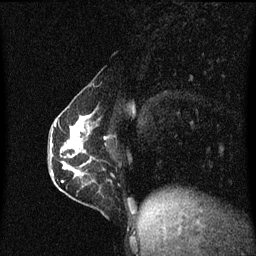
Breast MRI (dynamic contrast-enhanced), one sagittal slice; slice 24 of 60 in the series (ordered by position); dynamic contrast-enhanced series, image 2 of 3 at this slice position (ordered by acquisition); 1.5 T; TE 4.2 ms, TR 8.4 ms; 2 mm slice thickness; 256 × 256 image matrix. Patient: female, 40 years.
Outlined on this slice (semi-automatically segmented with operator editing):
- analysis volume of interest (the breast-tissue region the enhancement analysis was run in; not a lesion): box from (x=57, y=110) to (x=112, y=191) px
- tumour enhancement mask (voxels above the 70 % enhancement threshold inside the analysis volume of interest): (x=60, y=112)–(x=94, y=183)